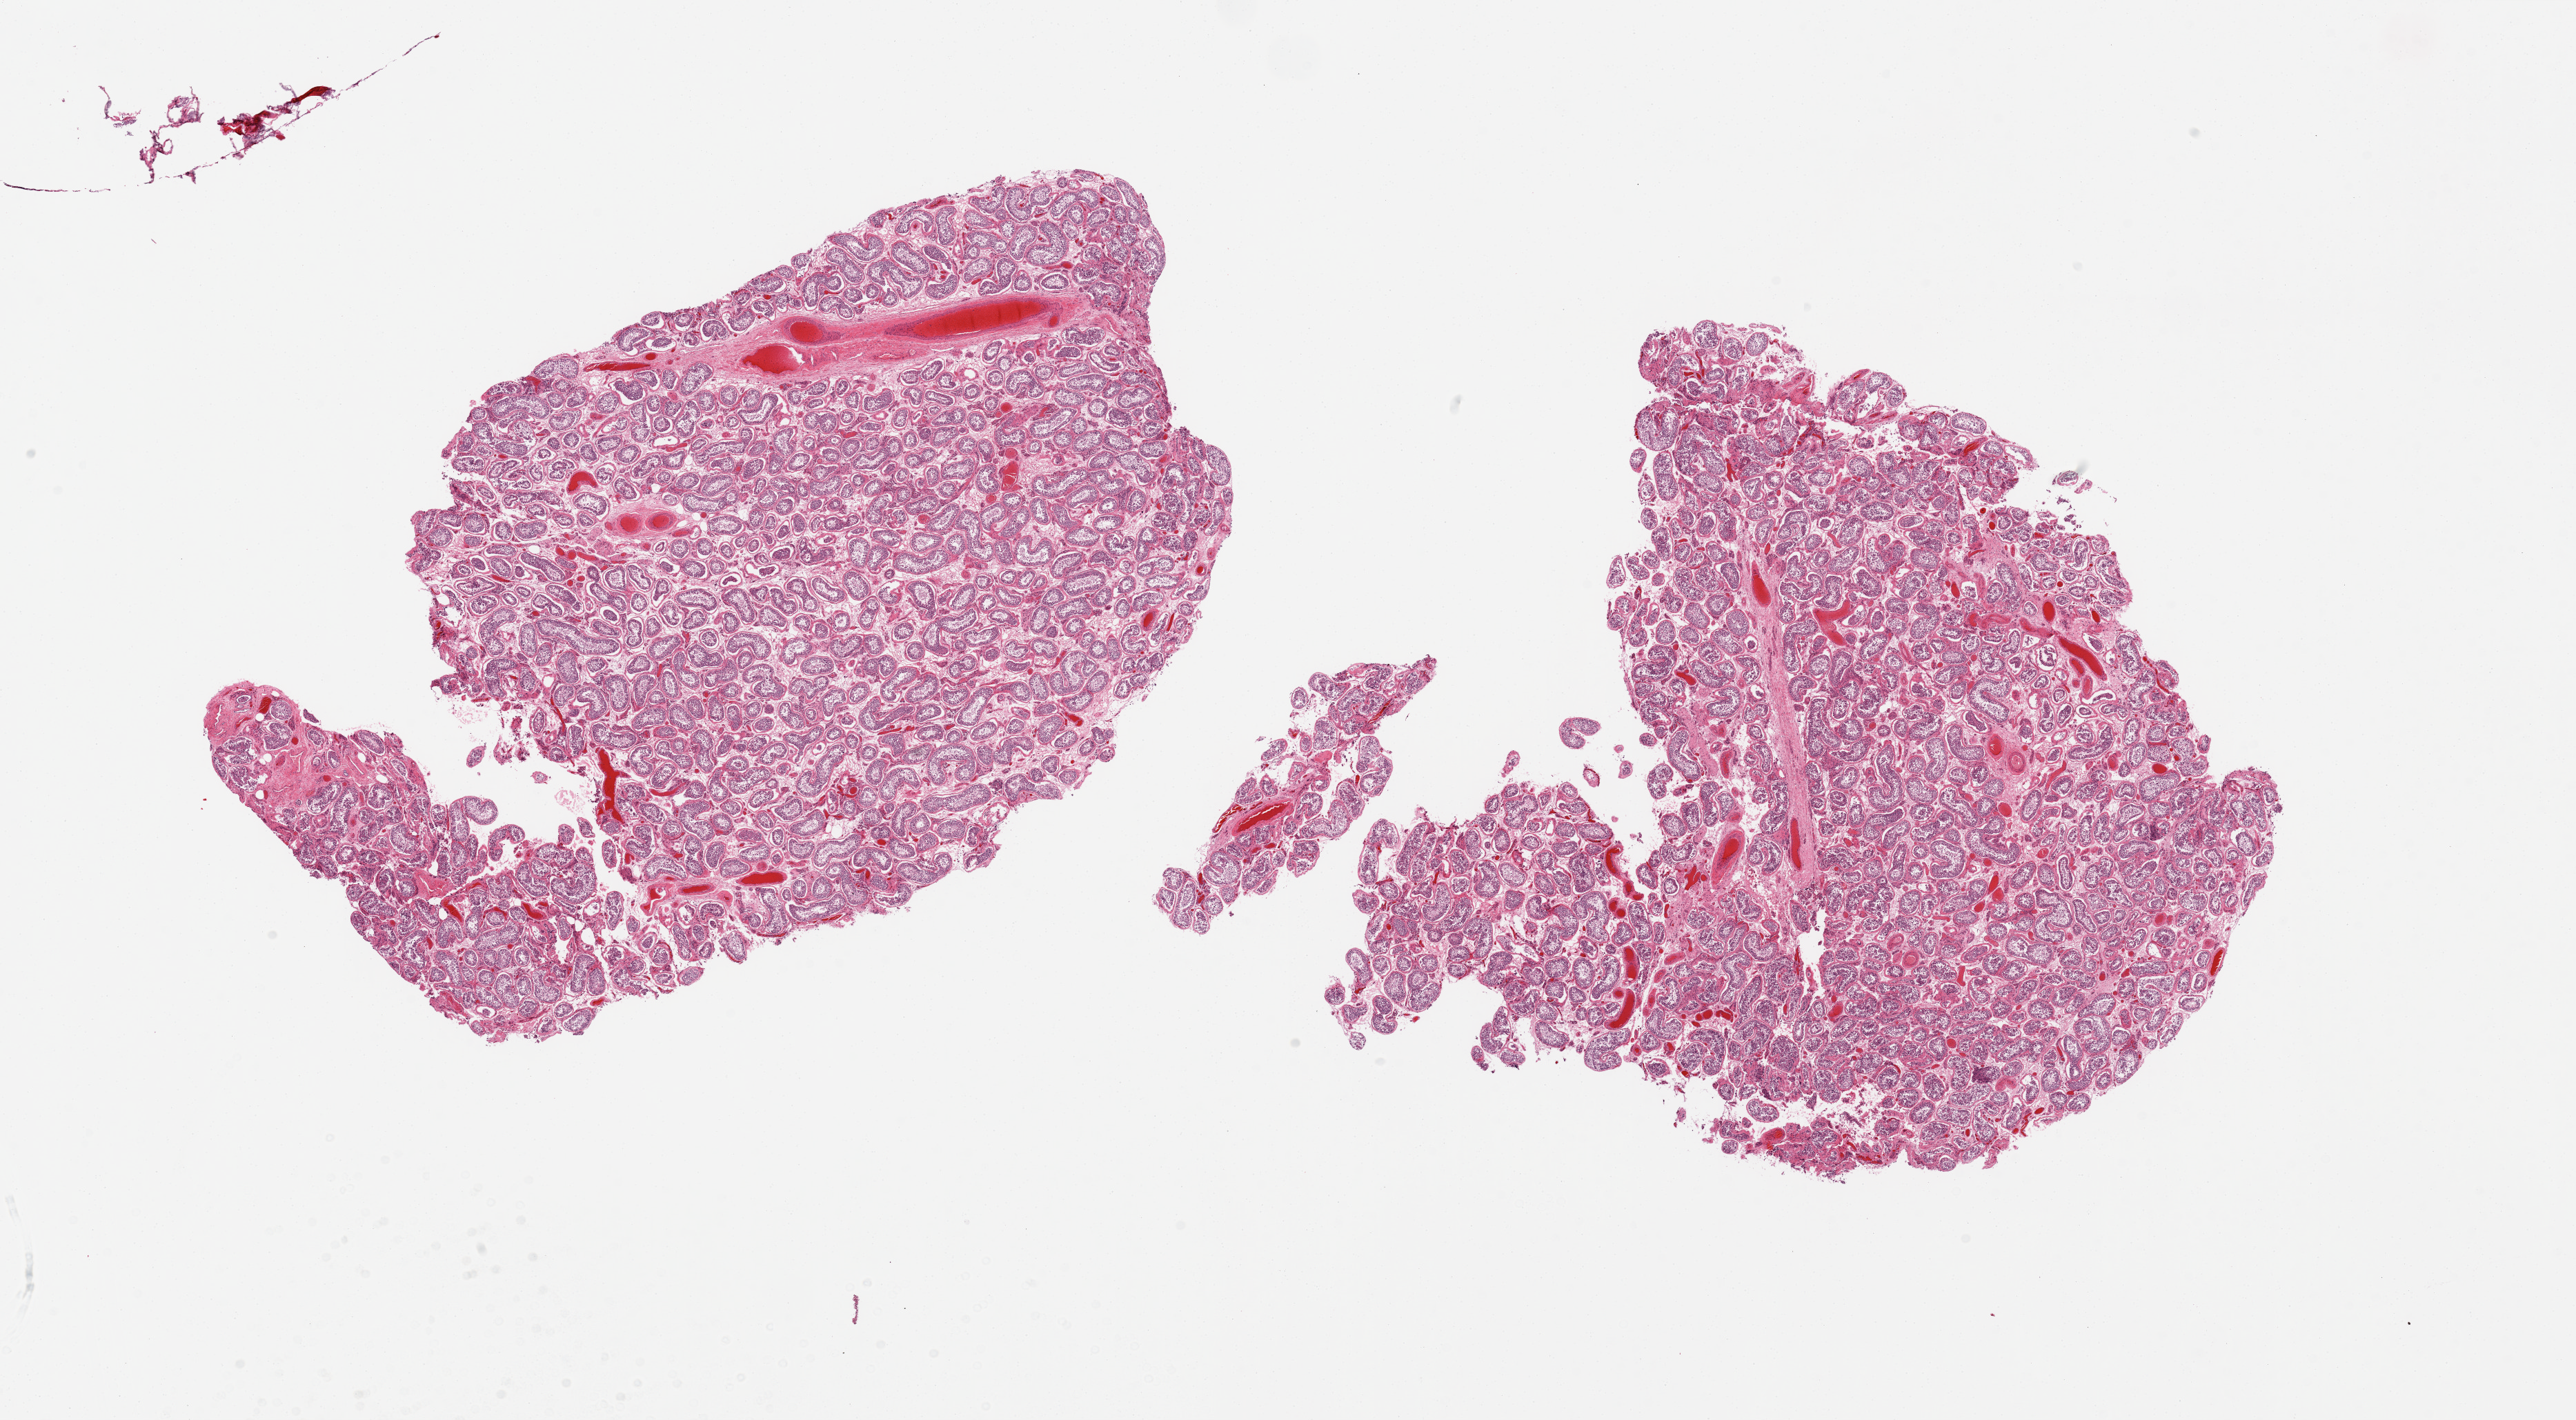
Digitized H&E-stained section, low-resolution overview of the scanned area, about 29.5 x 16.3 mm. PAXgene-fixed, paraffin-embedded tissue. Section of testis (target tissue). Tissue donor sample. Male donor.
Pathologist's review note for this sample: 2 pieces, active spermatogenesis.